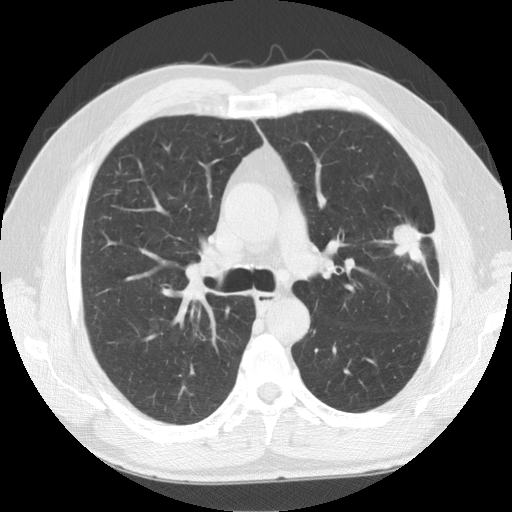
Low-dose screening chest CT, one axial slice. Slice 95 of 141 in the series (ordered by position). 120 kVp. Lung window (W 1500 / L -600 HU). 512 × 512 image matrix, field of view 360 × 360 mm.
Annotated regions visible in this slice (outlined manually by an expert reader):
- lesion 1 (tumor, upper lobe of left lung): bounding box <391,224,425,263> (left, top, right, bottom; pixels)